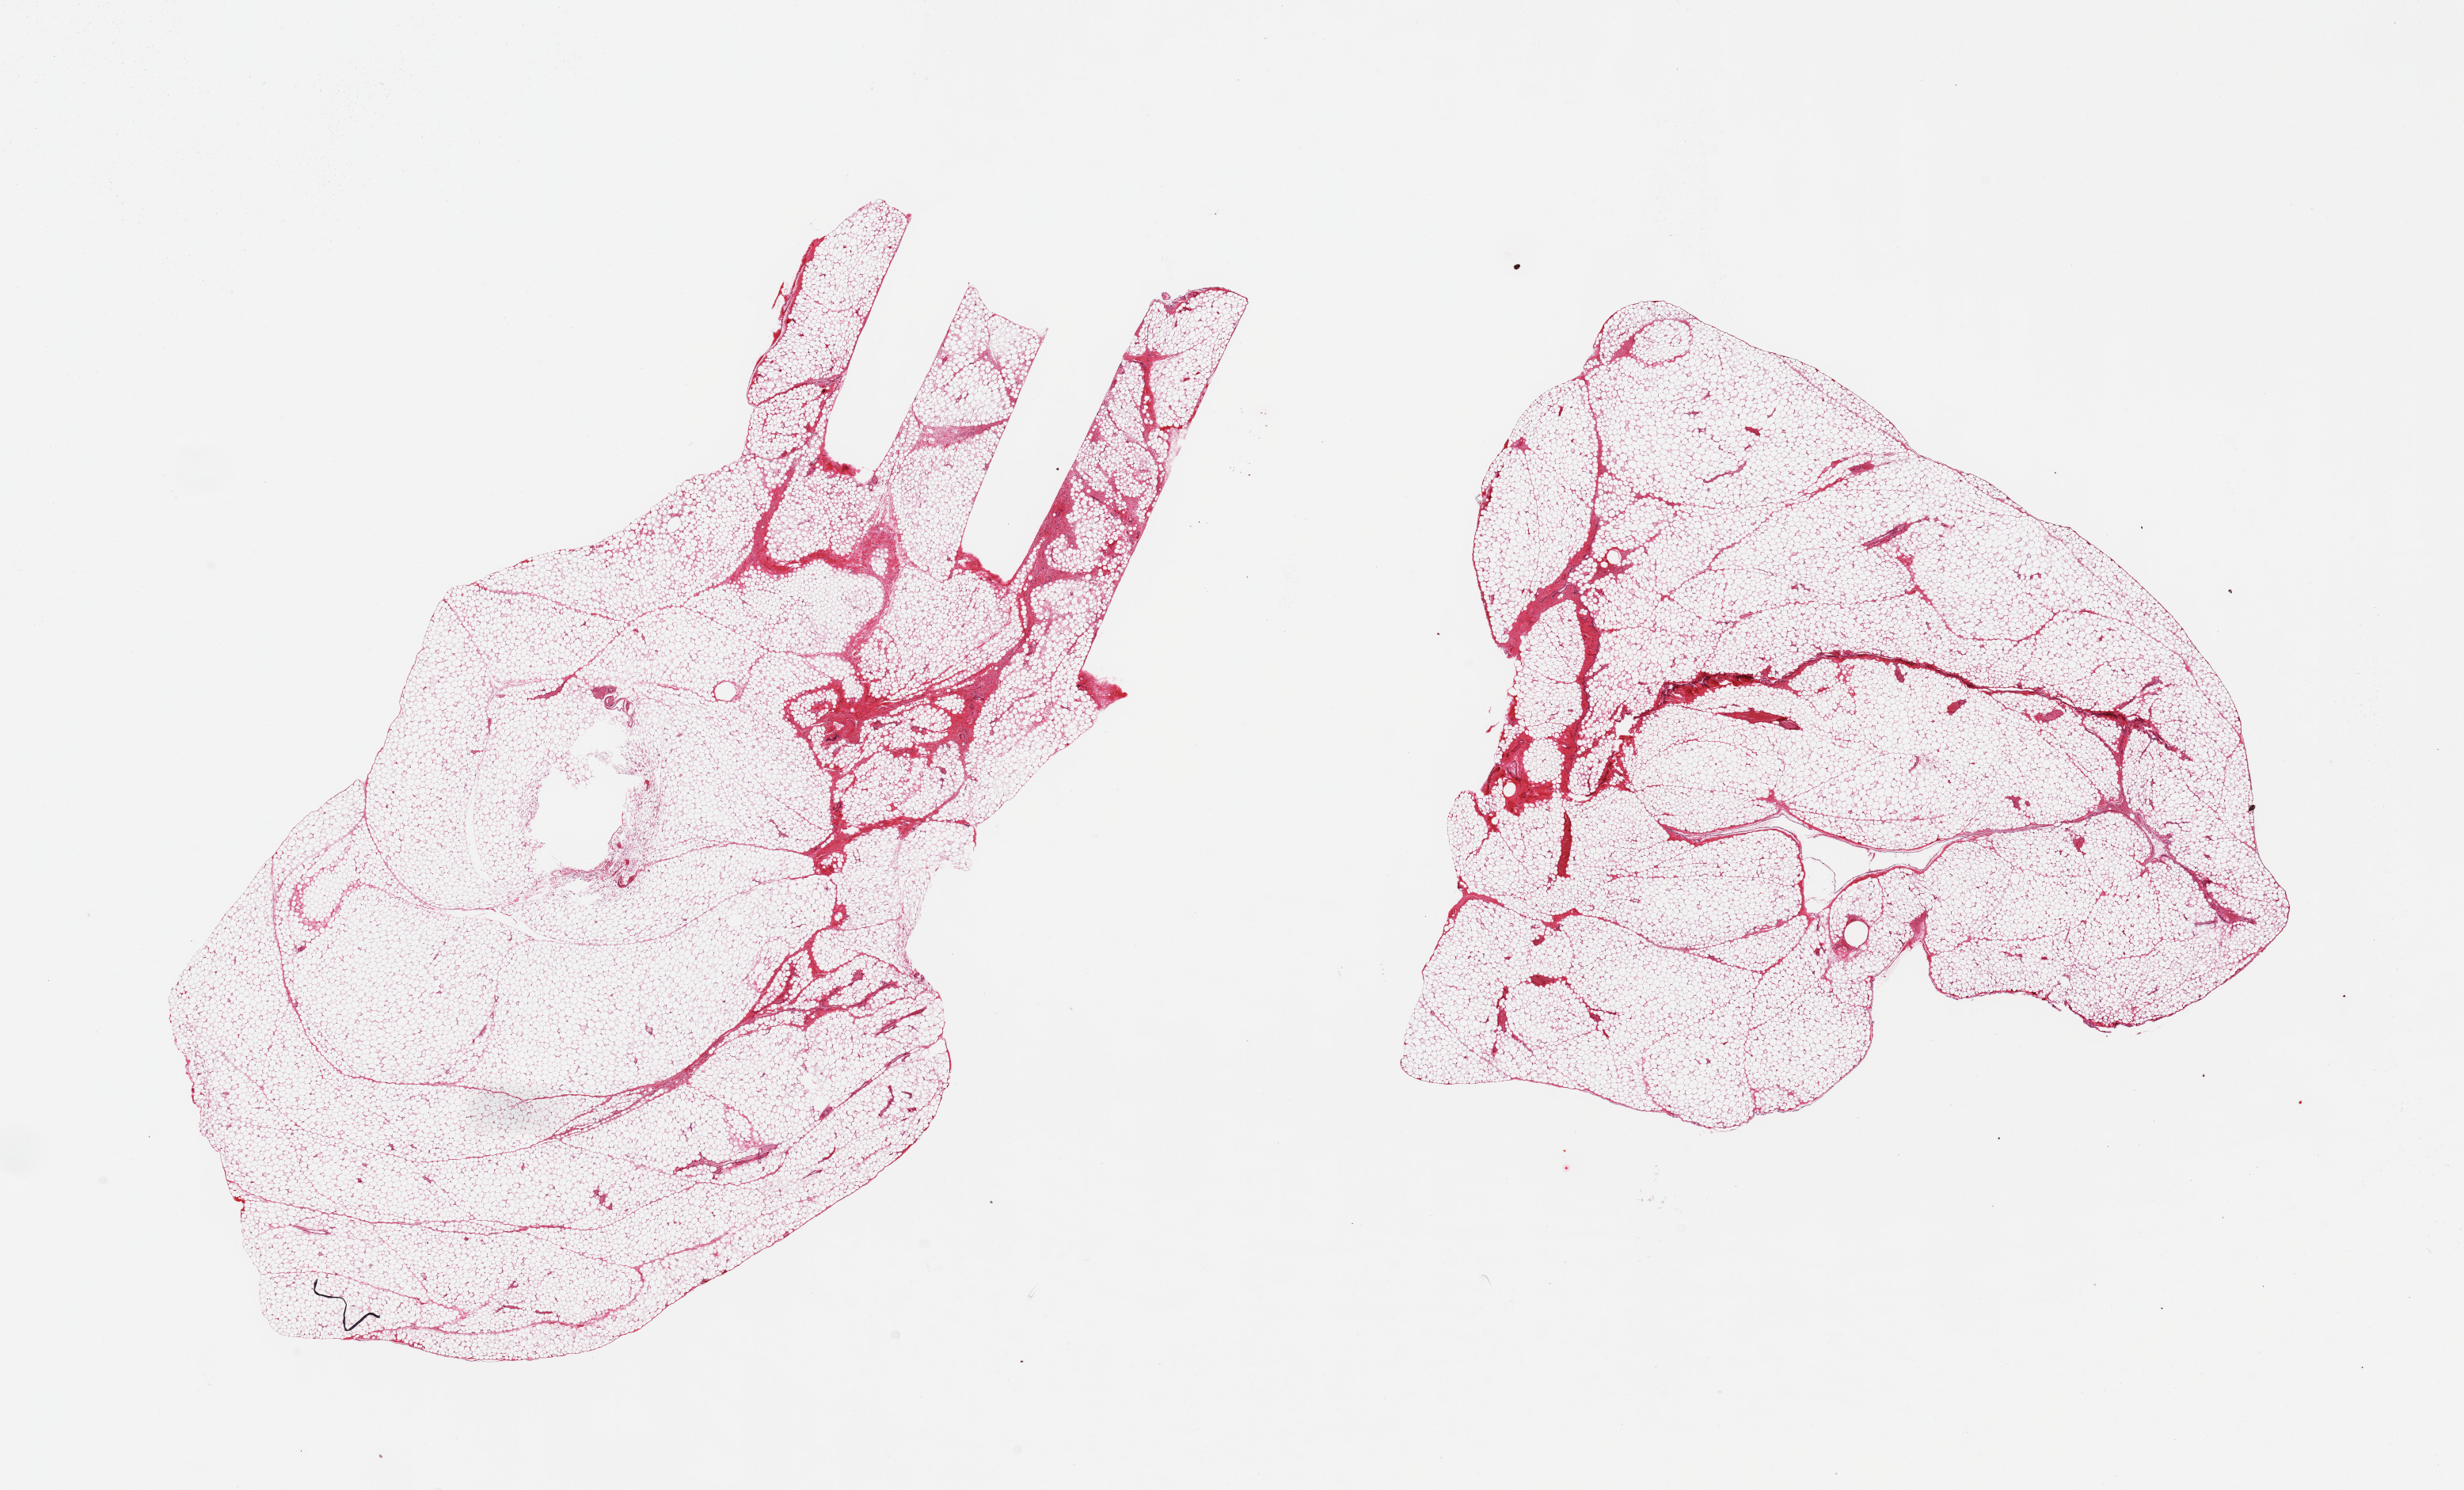
Digitized H&E-stained section, low-resolution overview of the scanned area, about 24.6 x 14.9 mm, PAXgene-fixed paraffin-embedded (PFPE) section, section of omentum (target tissue), donor tissue sample. Male donor.
Pathologist's review note for this sample: 2 pieces; <5% fibrous content.